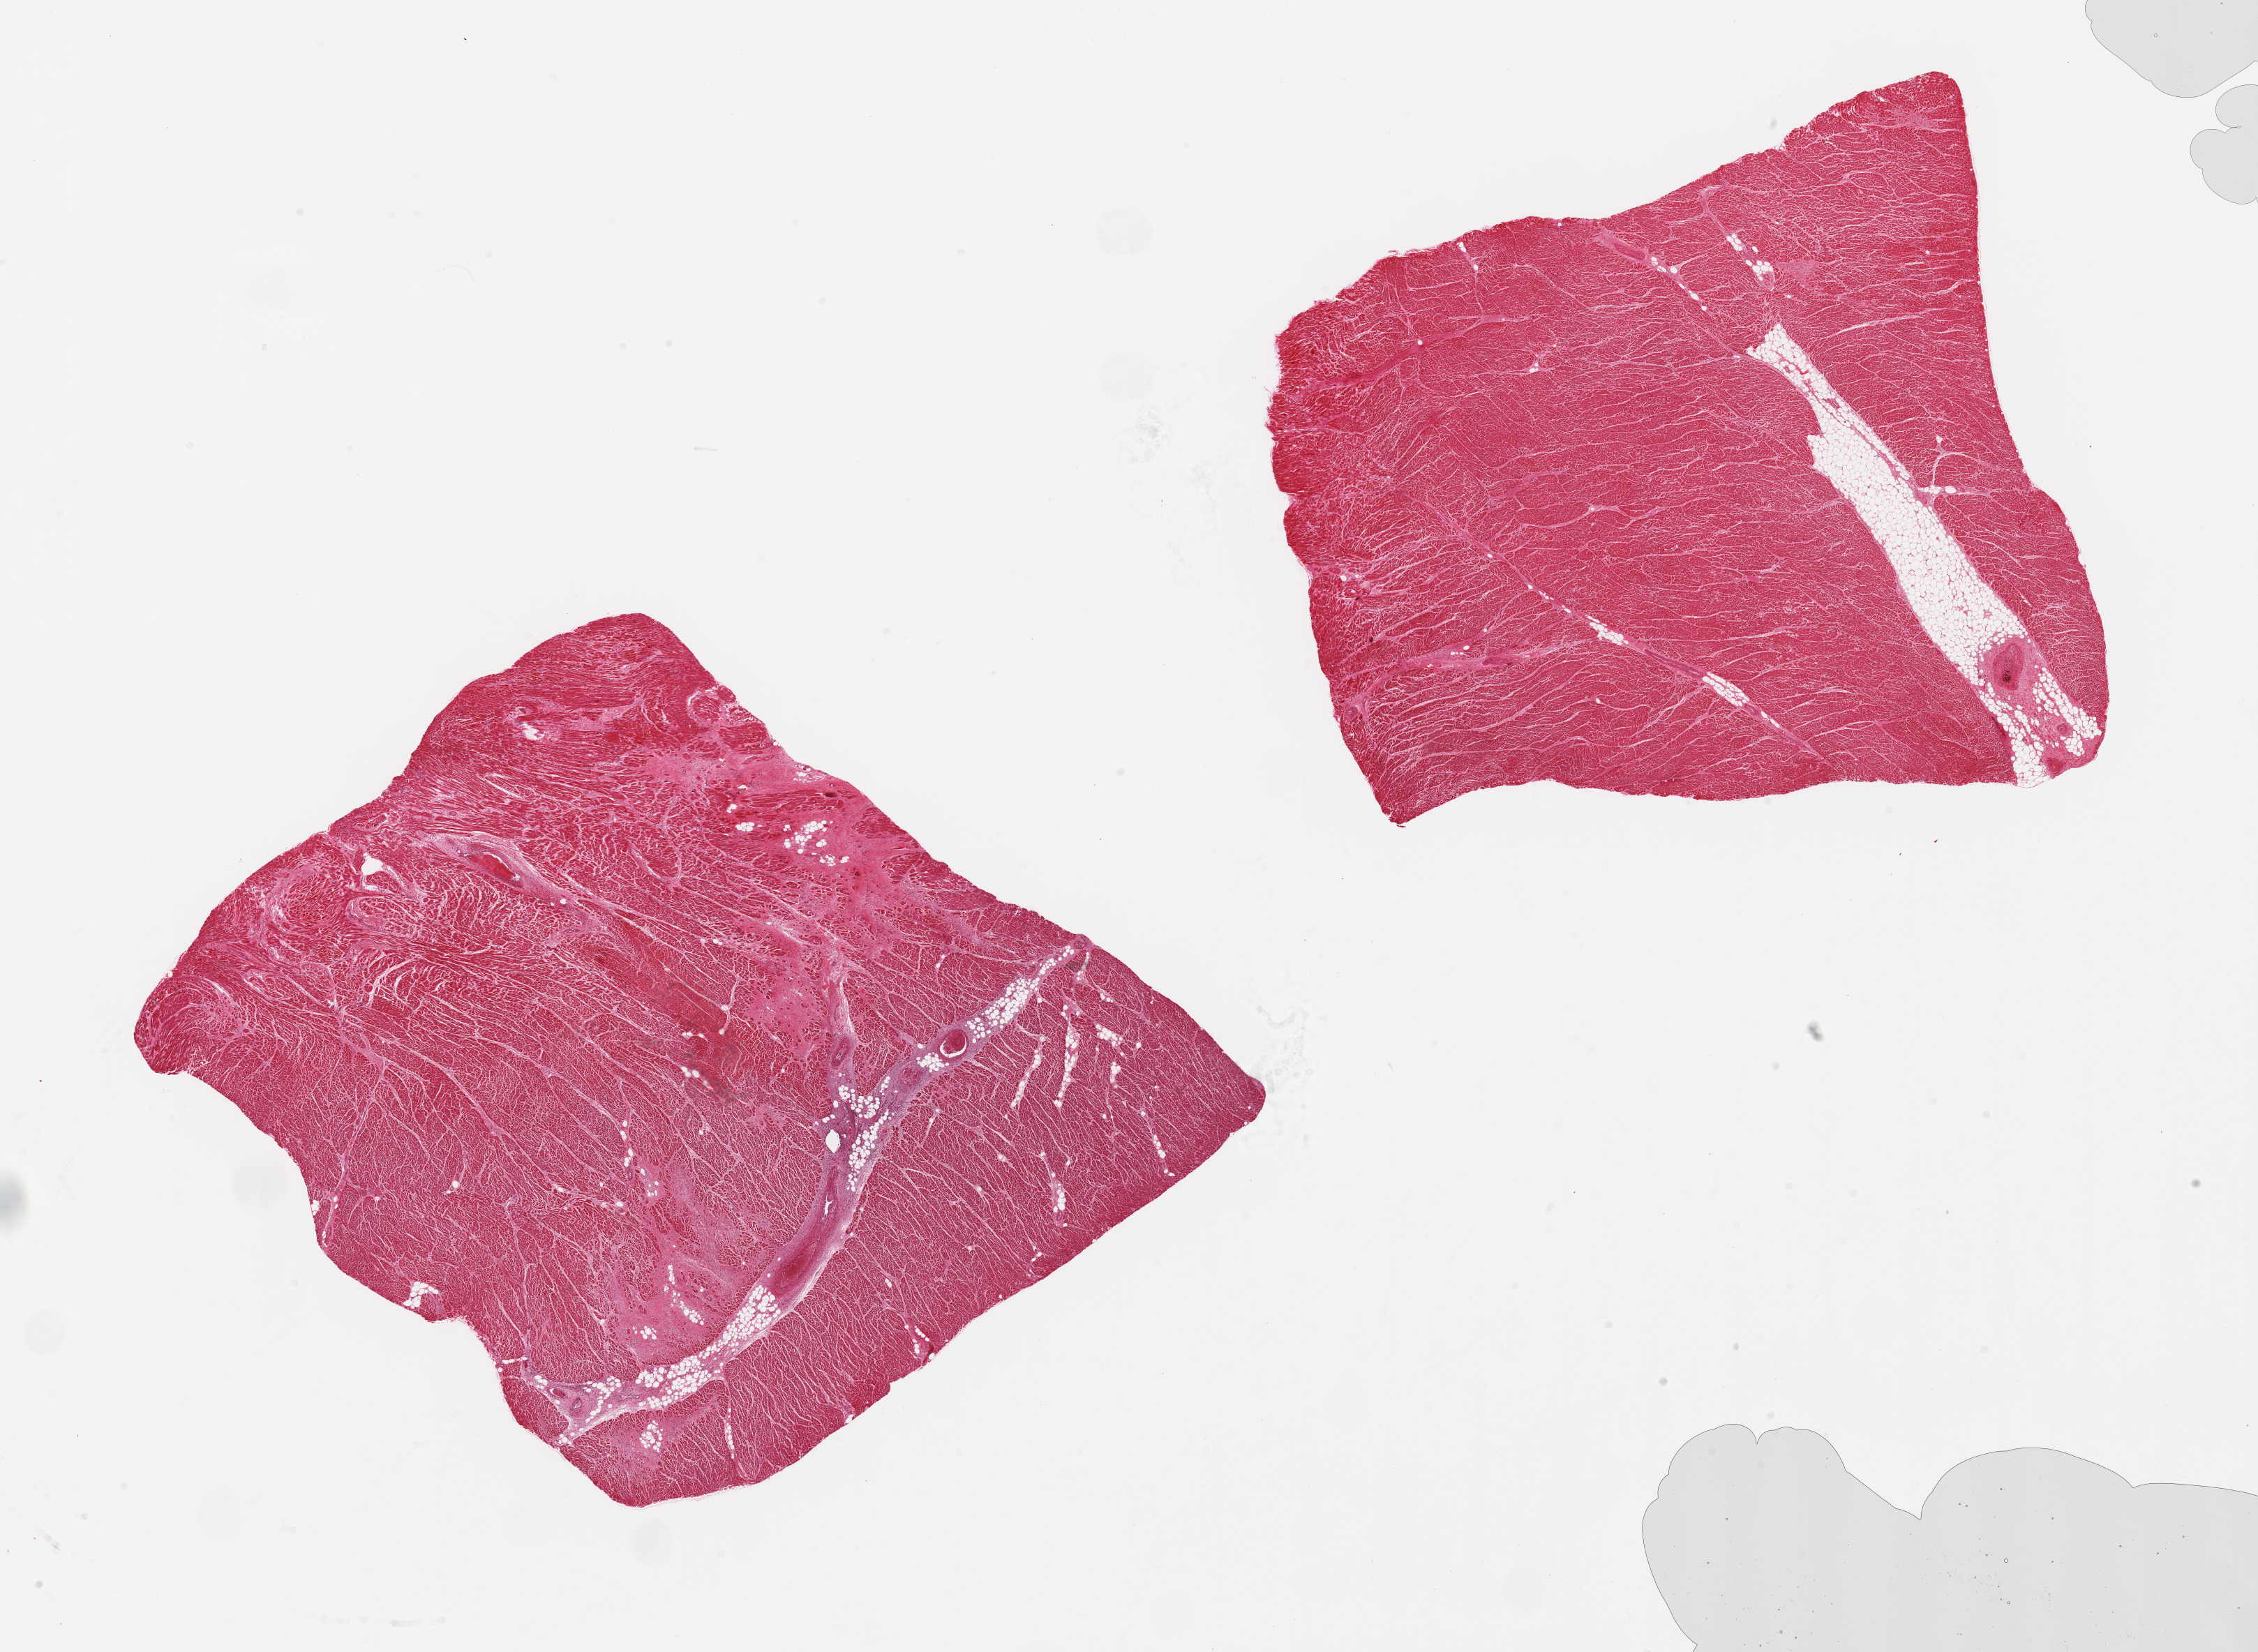
Digitized hematoxylin and eosin (H&E)-stained section, brightfield — low-resolution overview of the scanned area, about 25.6 x 18.7 mm (from a 20x scan). PAXgene-fixed paraffin-embedded (PFPE) section. Section of heart (target tissue). Donor tissue sample.
Review note (as recorded): 2 pieces chronic (, remote infarct) and subacute ischemic damage.